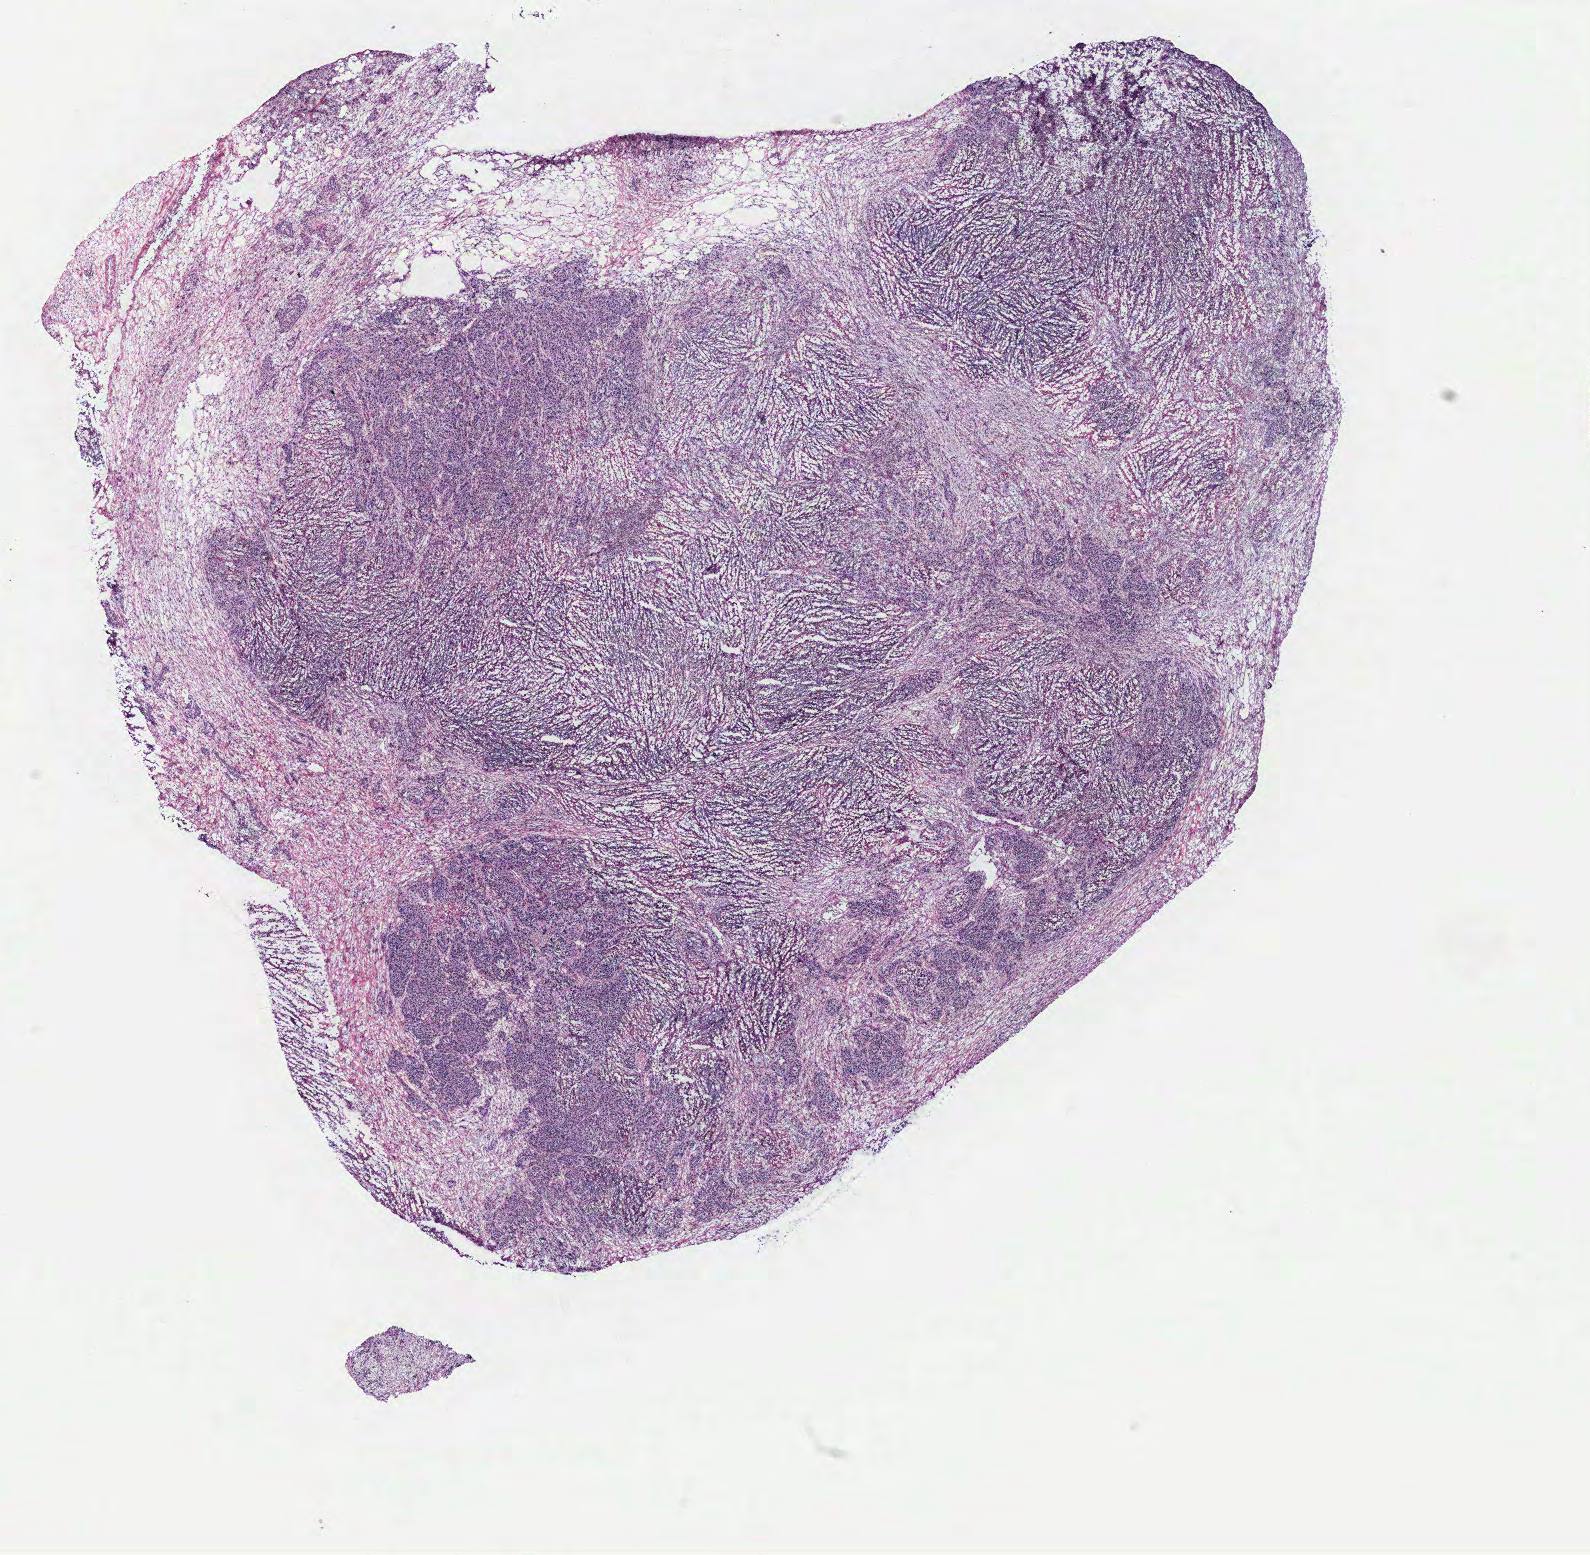
H&E whole-slide image, shown as a low-resolution overview of the whole scanned area (about 12.7 x 12.4 mm, slide scanned at 40x), ovary, tissue type not recorded. Female patient.
- patient diagnosis: Serous adenocarcinoma, NOS